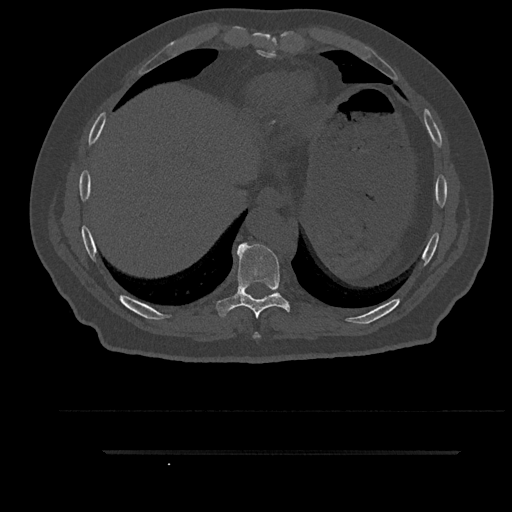
CT including the spine, one axial slice; slice 424 of 797 in the series (ordered by position); reconstruction kernel Br40s/3; 120 kVp; bone window (W 1800 / L 400 HU); 0.5 mm slice thickness; 512 × 512 image matrix. Male patient, age 63 years. Case-level facts recorded for this patient, not image findings: primary cancer: renal; vertebrae with lytic lesions (as recorded): T8.
Annotated regions visible in this slice (semi-automatic segmentation, software-assisted and operator-edited):
- T8 vertebra: bounding box <253,332,260,338> (left, top, right, bottom; pixels)
- T9 vertebra: <215,242,294,319>